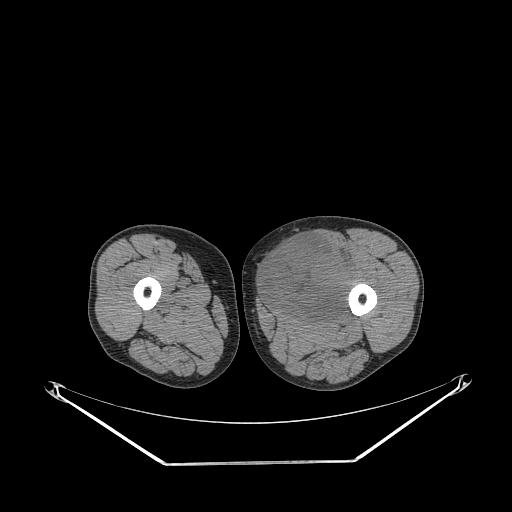
CT of an extremity soft-tissue mass (from a PET/CT study), one axial slice. Reconstruction kernel STANDARD. Soft-tissue window (W 400 / L 40 HU). 512 × 512 image matrix, field of view 500 × 500 mm. Male patient. Case-level facts recorded for this patient, not image findings: histological type: pleiomorphic liposarcoma; grade: high; site of the primary tumour: left thigh.
Outlined on this slice (expert contour drawn on MRI and transferred to this co-registered scan by the dataset authors):
- gross tumour volume including surrounding oedema: box from (x=263, y=235) to (x=357, y=320) px
- gross tumour volume (mass): (x=263, y=235)–(x=353, y=320)